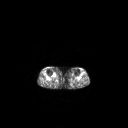
FDG PET of an extremity soft-tissue mass (from a PET/CT study), one axial slice; 3.27 mm slice thickness; 128 × 128 image matrix, field of view 700 × 700 mm. Patient: female, 65 years. Case-level facts recorded for this patient, not image findings: histological type: undifferentiated – high grade; grade: high; site of the primary tumour: right thigh.
Outlined on this slice (expert contour drawn on MRI and transferred to this co-registered scan by the dataset authors):
- gross tumour volume (mass): bounding box [x1, y1, x2, y2] px = [53, 73, 56, 76]